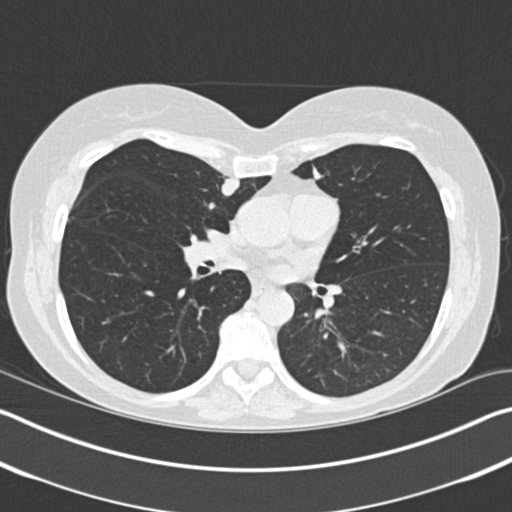
Axial slice from a low-dose chest CT screening exam; baseline screening round; lung window (W 1500 / L -600 HU); 2 mm slice thickness; slice 88 of 183 in the series. Female, age 61 years at enrolment.
Lesion marked by an expert reader, bounding box (x1, y1, x2, y2) in pixels: (201, 169, 249, 211). The screening reader recorded 2 non-calcified nodules or masses ≥4 mm on this exam (right upper lobe, right upper lobe); which of them this box marks is not recorded. Later outcome: lung cancer diagnosed 131 days after this screen — adenocarcinoma, NOS, right upper lobe, stage IA (AJCC 6th edition), 11 mm at pathology.